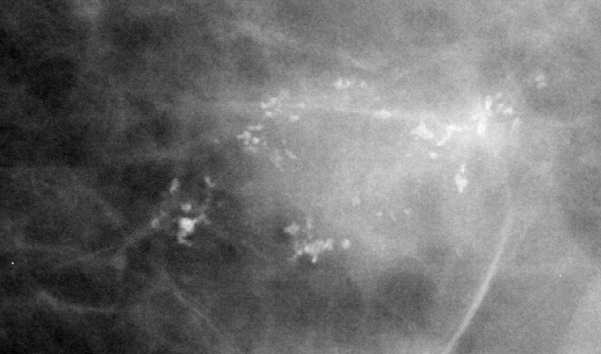
Crop from a digitized film mammogram around one marked abnormality, left breast, CC view, BI-RADS breast density category 3 (scale 1–4).
Finding: calcifications, morphology pleomorphic, distribution clustered / segmental; BI-RADS assessment category 4; subtlety rating 4 on a 1 (subtle) to 5 (obvious) scale; pathology result (as recorded, not read from the image): benign.